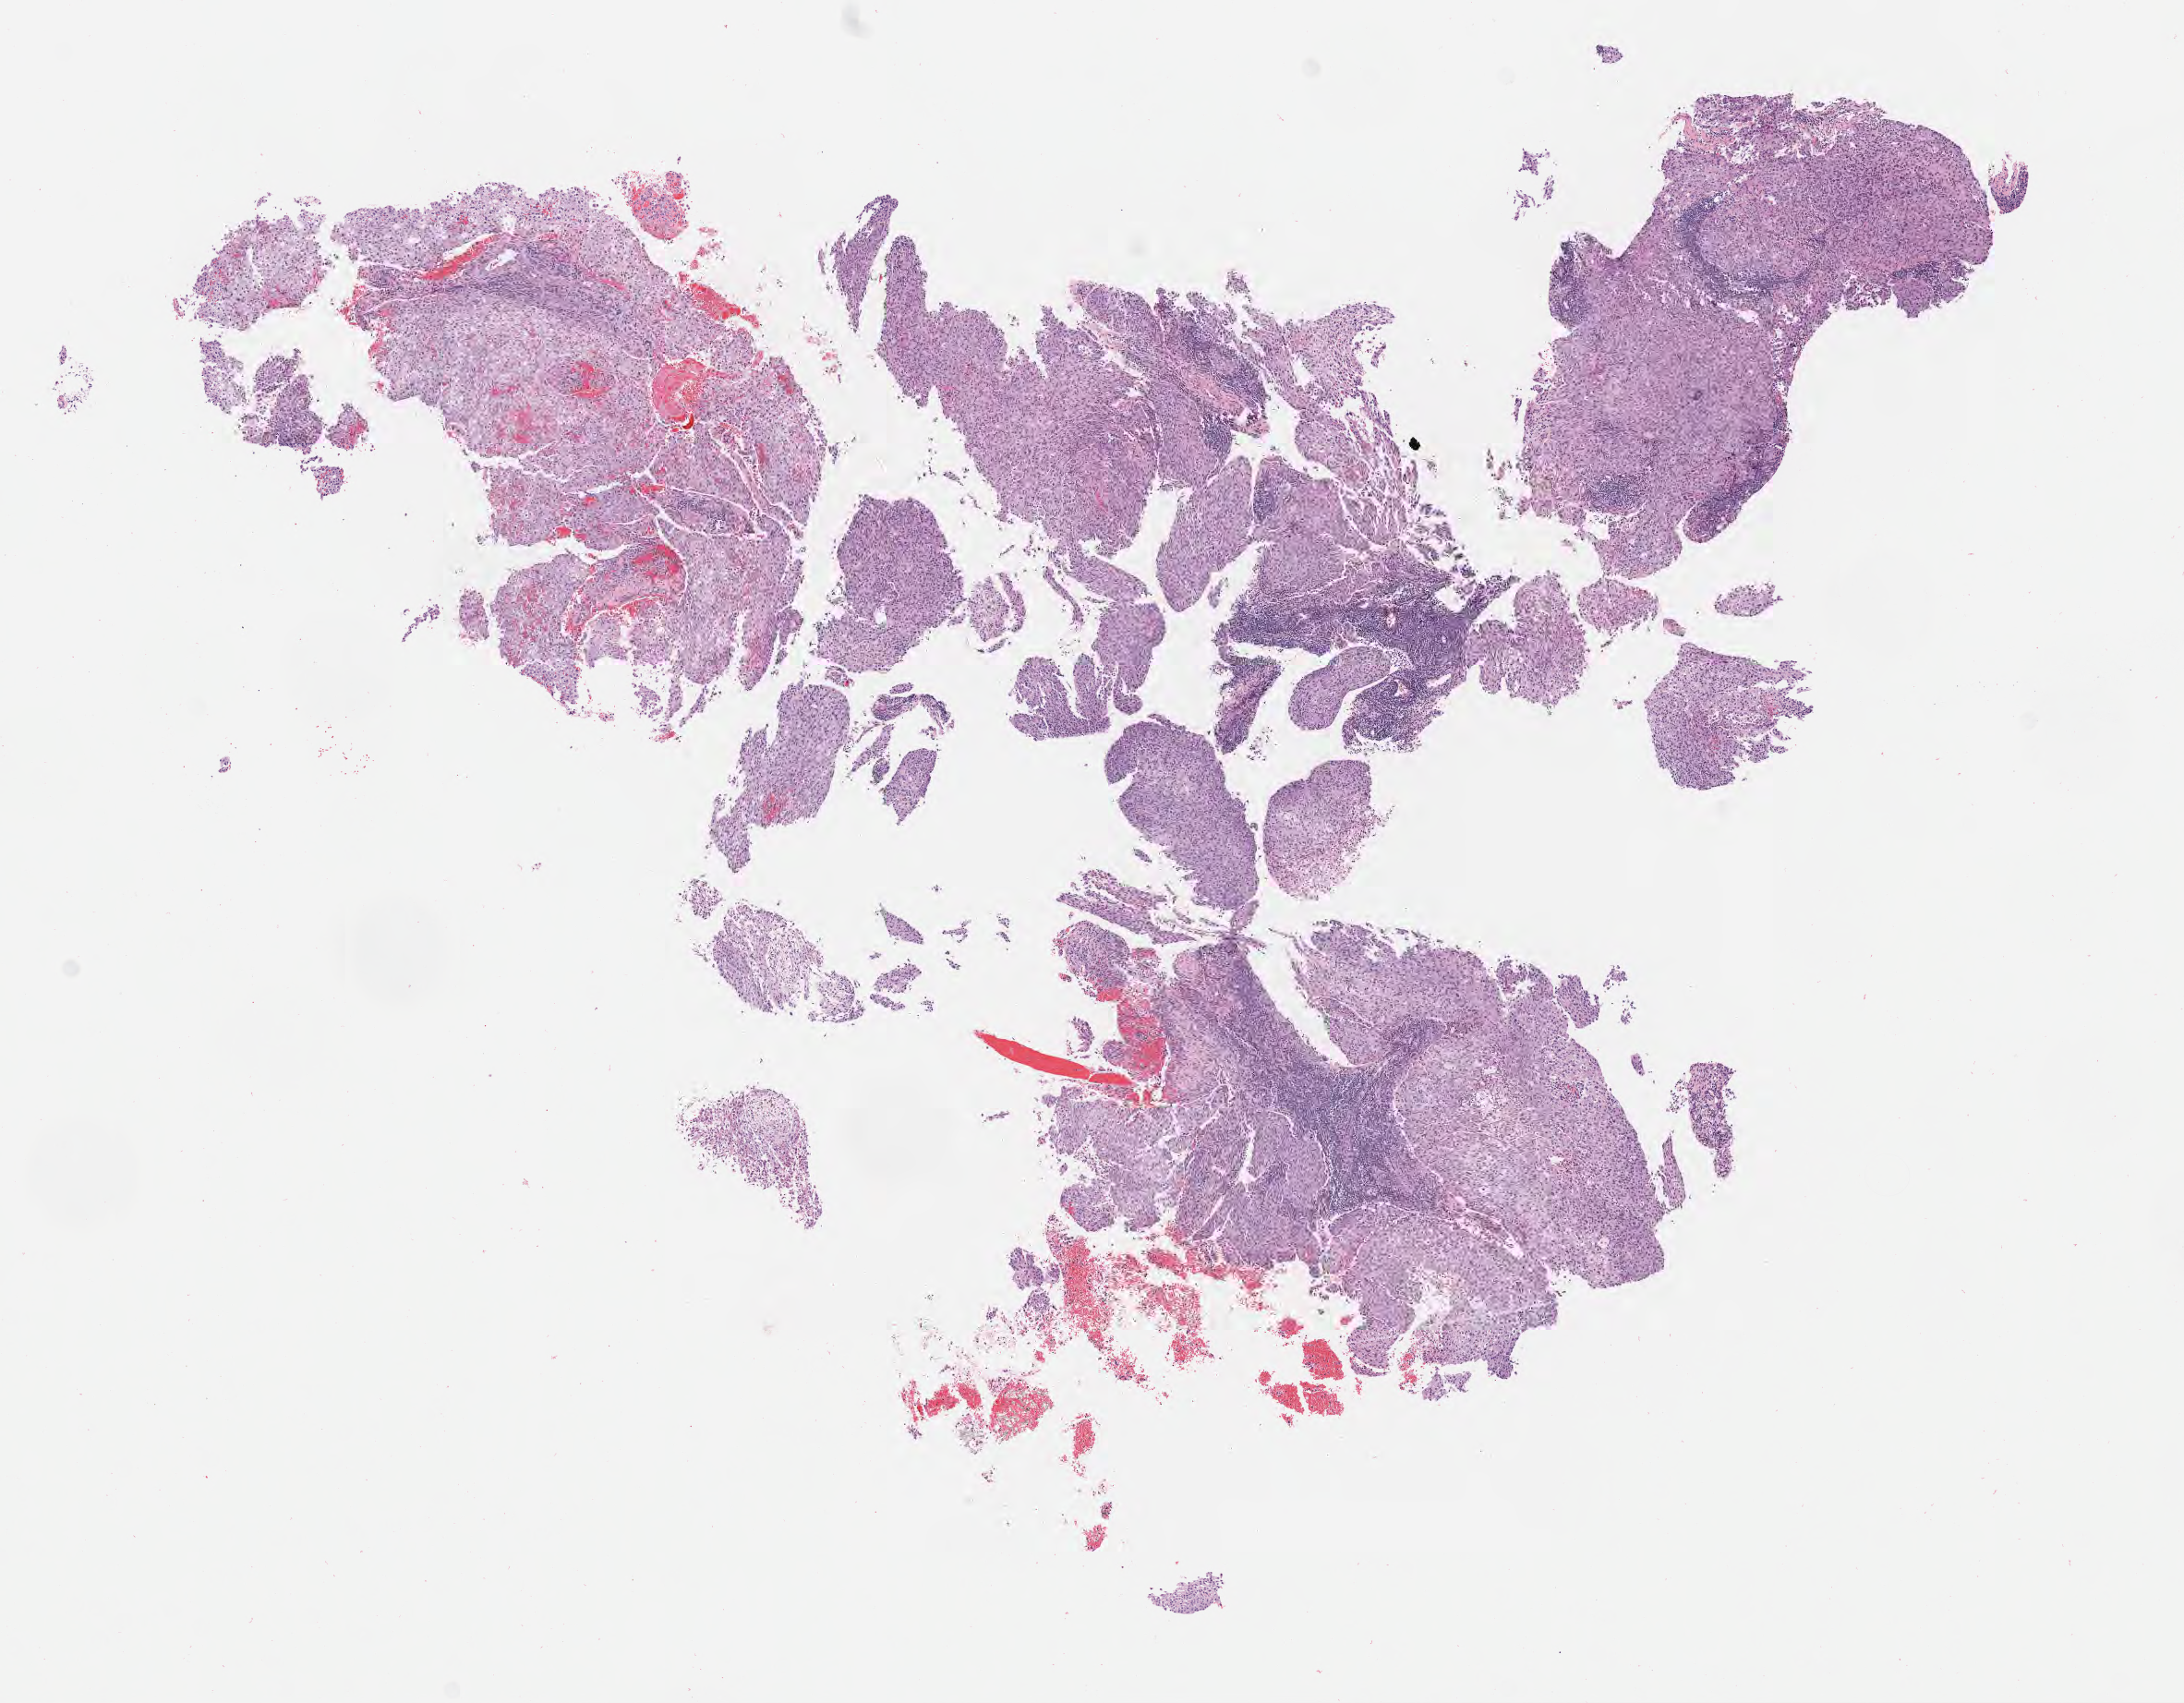
Whole-slide image, hematoxylin and eosin (H&E) stain, shown as a low-resolution overview of the whole scanned area (about 9.6 x 7.5 mm). Specimen: tumor tissue. Site: cervix. Patient: female, 57 years old.
Histologic diagnosis: Squamous cell carcinoma, large cell, nonkeratinizing, NOS.